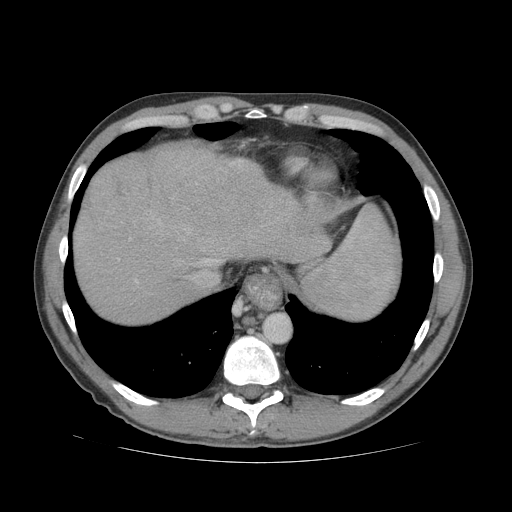
Contrast-enhanced abdominal CT (liver protocol), one axial slice; position 64 of 81 along the scan axis; reconstruction kernel STANDARD; 140 kVp; soft-tissue window (W 400 / L 40 HU); 512 × 512 image matrix. From the clinical record (not read from this slice): diagnosis: hepatocellular carcinoma (patient treated with transarterial chemoembolisation; whether this scan precedes or follows treatment is not stated here); TNM stage (as recorded): Stage-IVB; Child-Pugh class: B; tumour differentiation: well differentiated.
Annotated regions visible in this slice (semi-automatically segmented with operator editing):
- liver parenchyma outside the tumour (the mass and vessels are separate outlines, so this box may not span the whole liver): bounding box <72,144,304,322> (left, top, right, bottom; pixels)
- mass: <85,156,152,225>
- liver vessels: <135,163,234,282>